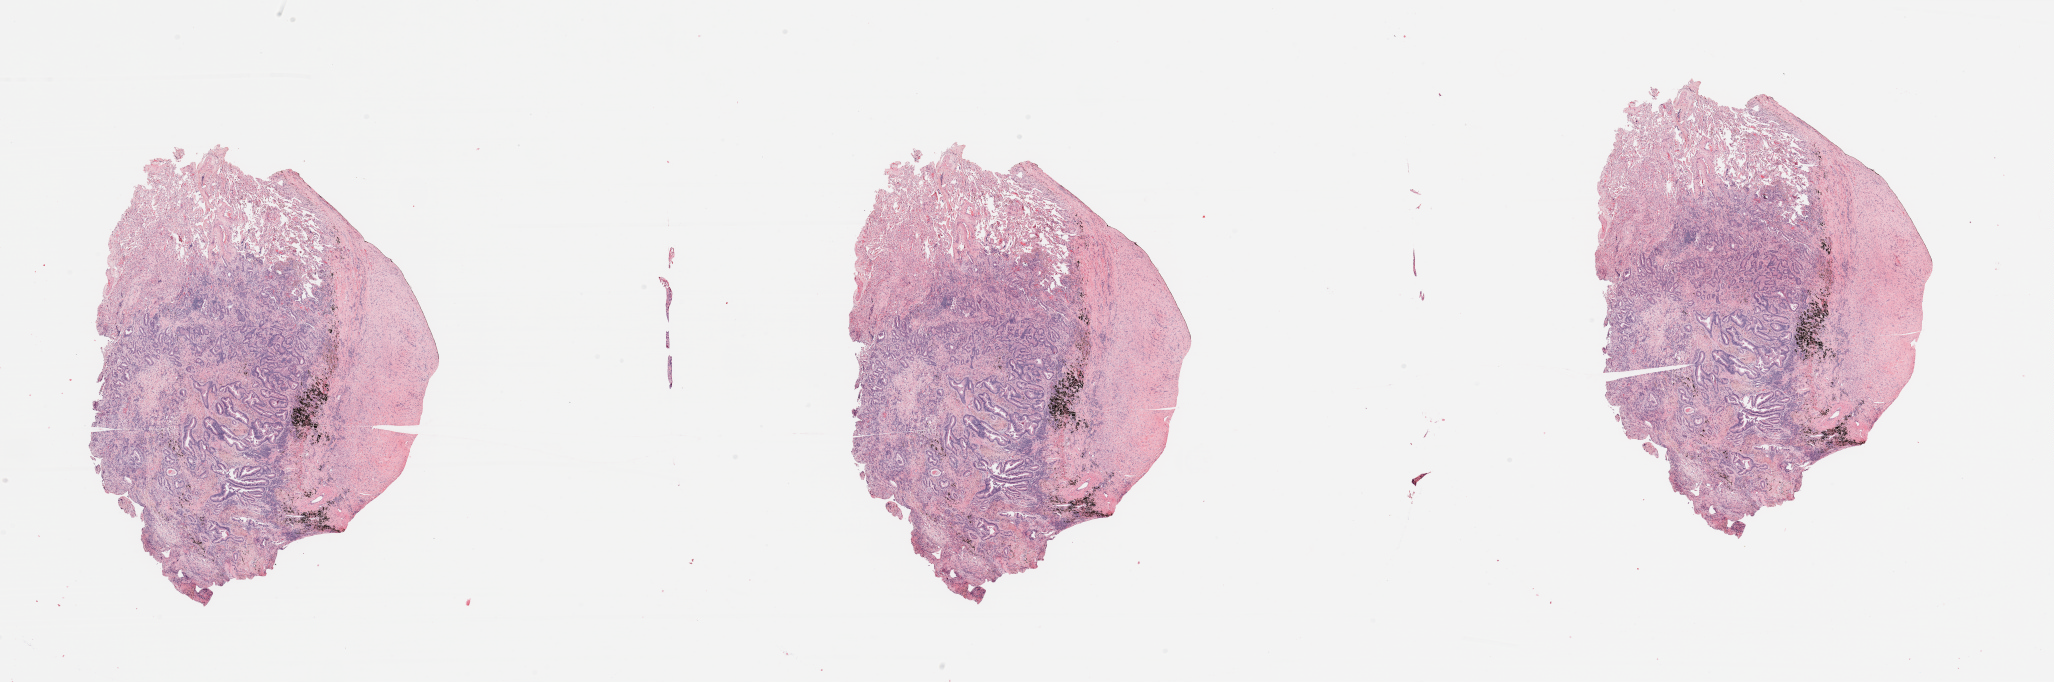
Whole-slide histology image, H&E — whole scanned area (about 32.5 x 10.8 mm, acquisition: 20x scan) shown as a low-resolution overview. Tumour tissue sample, sampled site: lung. 70-year-old female patient. Histologic grade: G1 (well differentiated). Pathologist review of this section (percent, as recorded): tumour nuclei 65%, necrosis 5%.
AJCC pathologic stage: IA. Primary tumour site (as recorded): right upper lobe. Diagnosis: Adenocarcinoma, NOS.